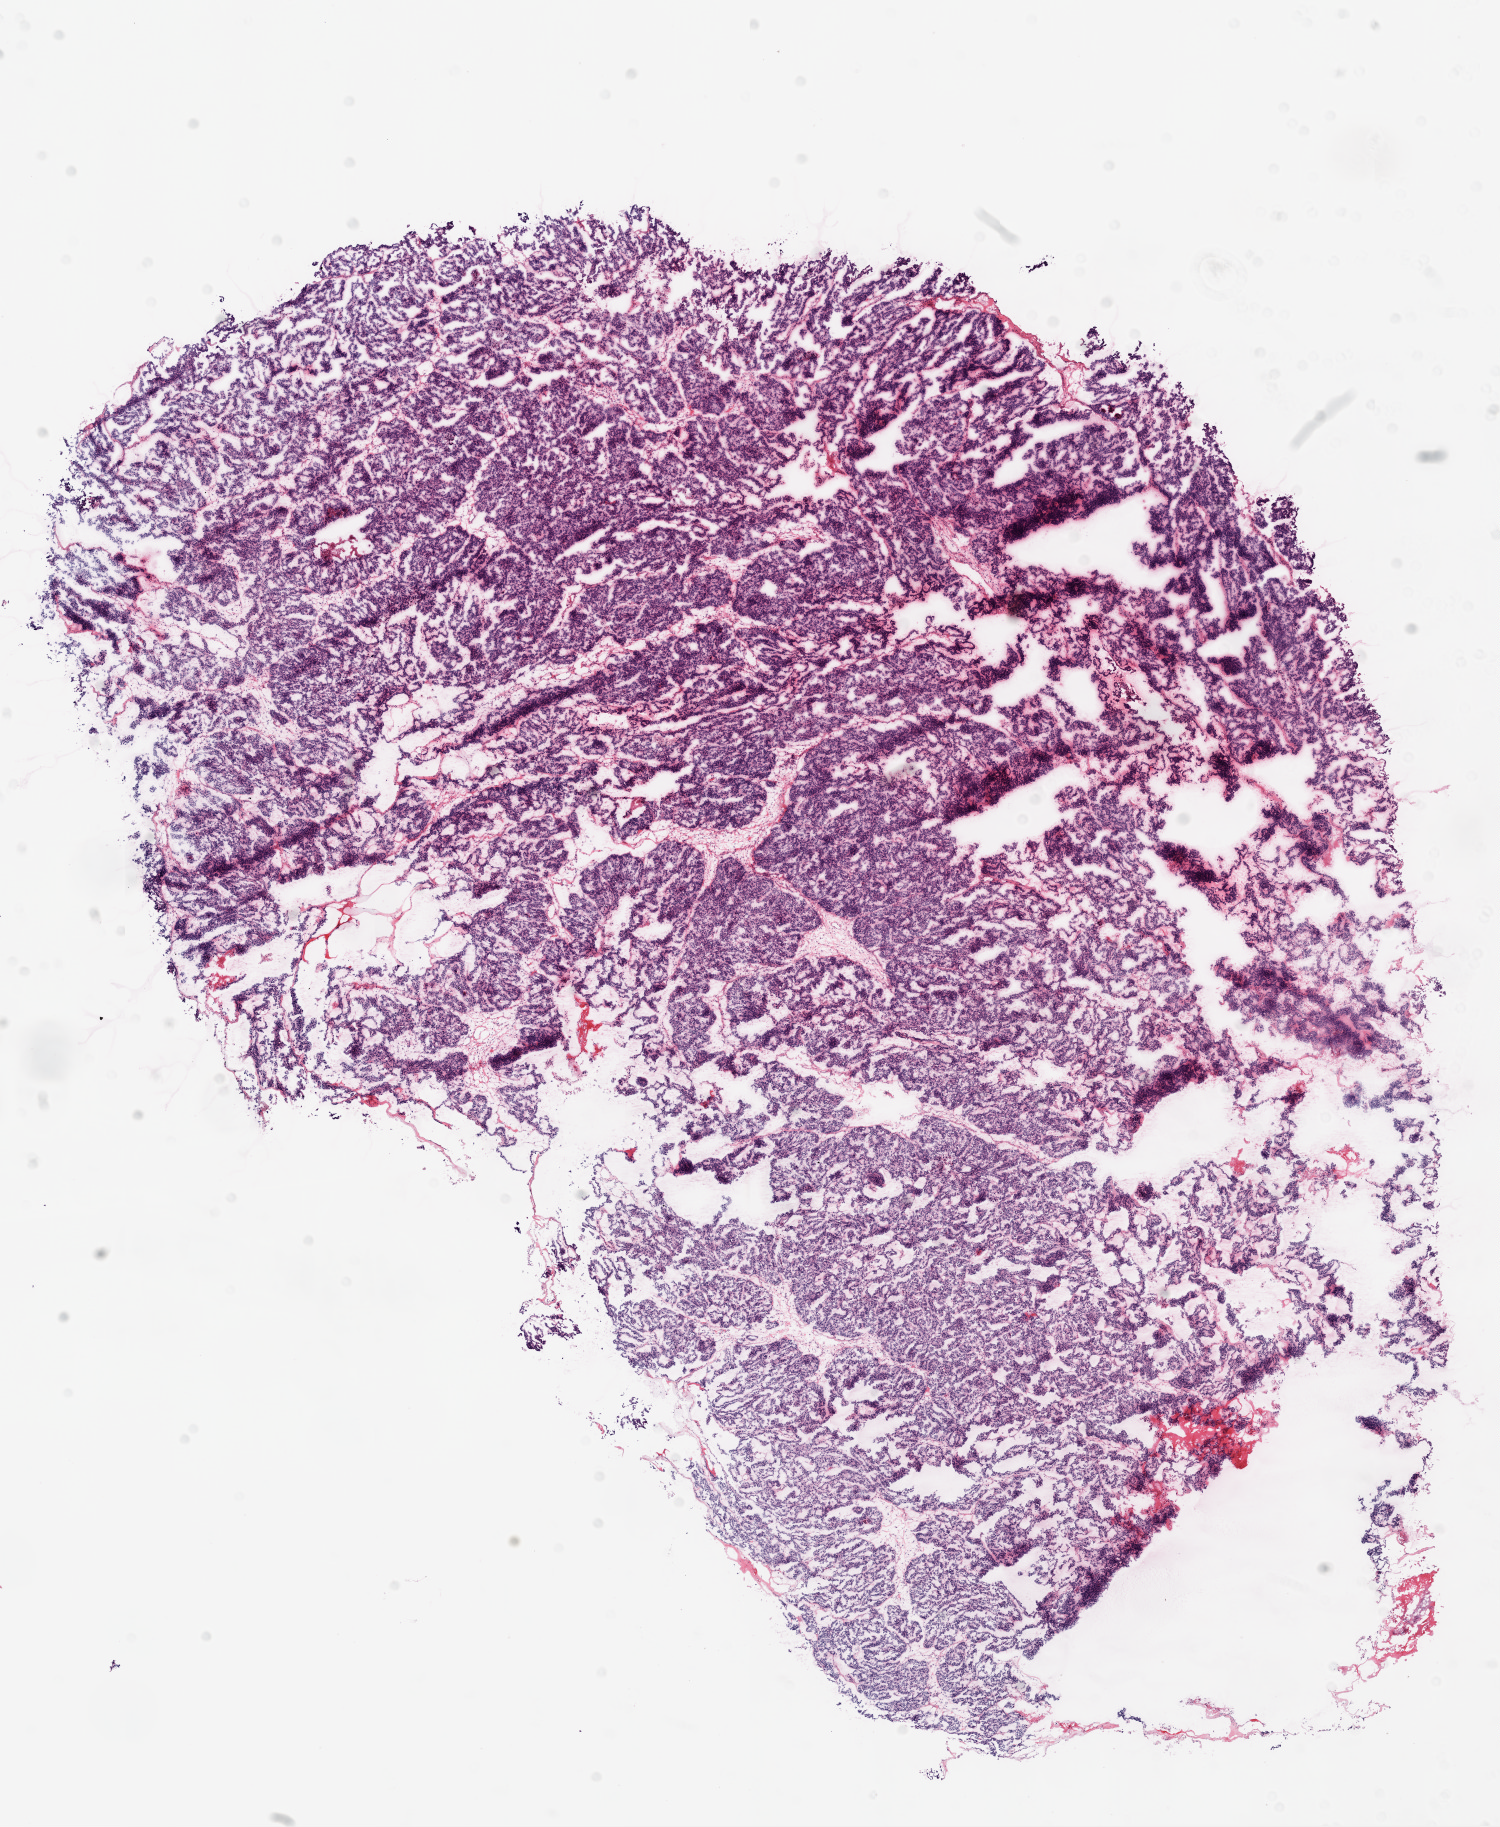
Hematoxylin and eosin (H&E) stained whole-slide image — whole scanned area (about 12.0 x 14.7 mm, from a 20x scan) shown as a low-resolution overview; frozen section; ovary, primary tumour sample. Female patient; age at initial diagnosis 51 years. Histologic grade: G3 (poorly differentiated). Composition of this section per pathologist review: tumour cells 95%, tumour nuclei 95%, normal cells 0%, stromal cells 5%, necrosis 0%.
* diagnosis: Serous cystadenocarcinoma, NOS
* FIGO stage: IIIC